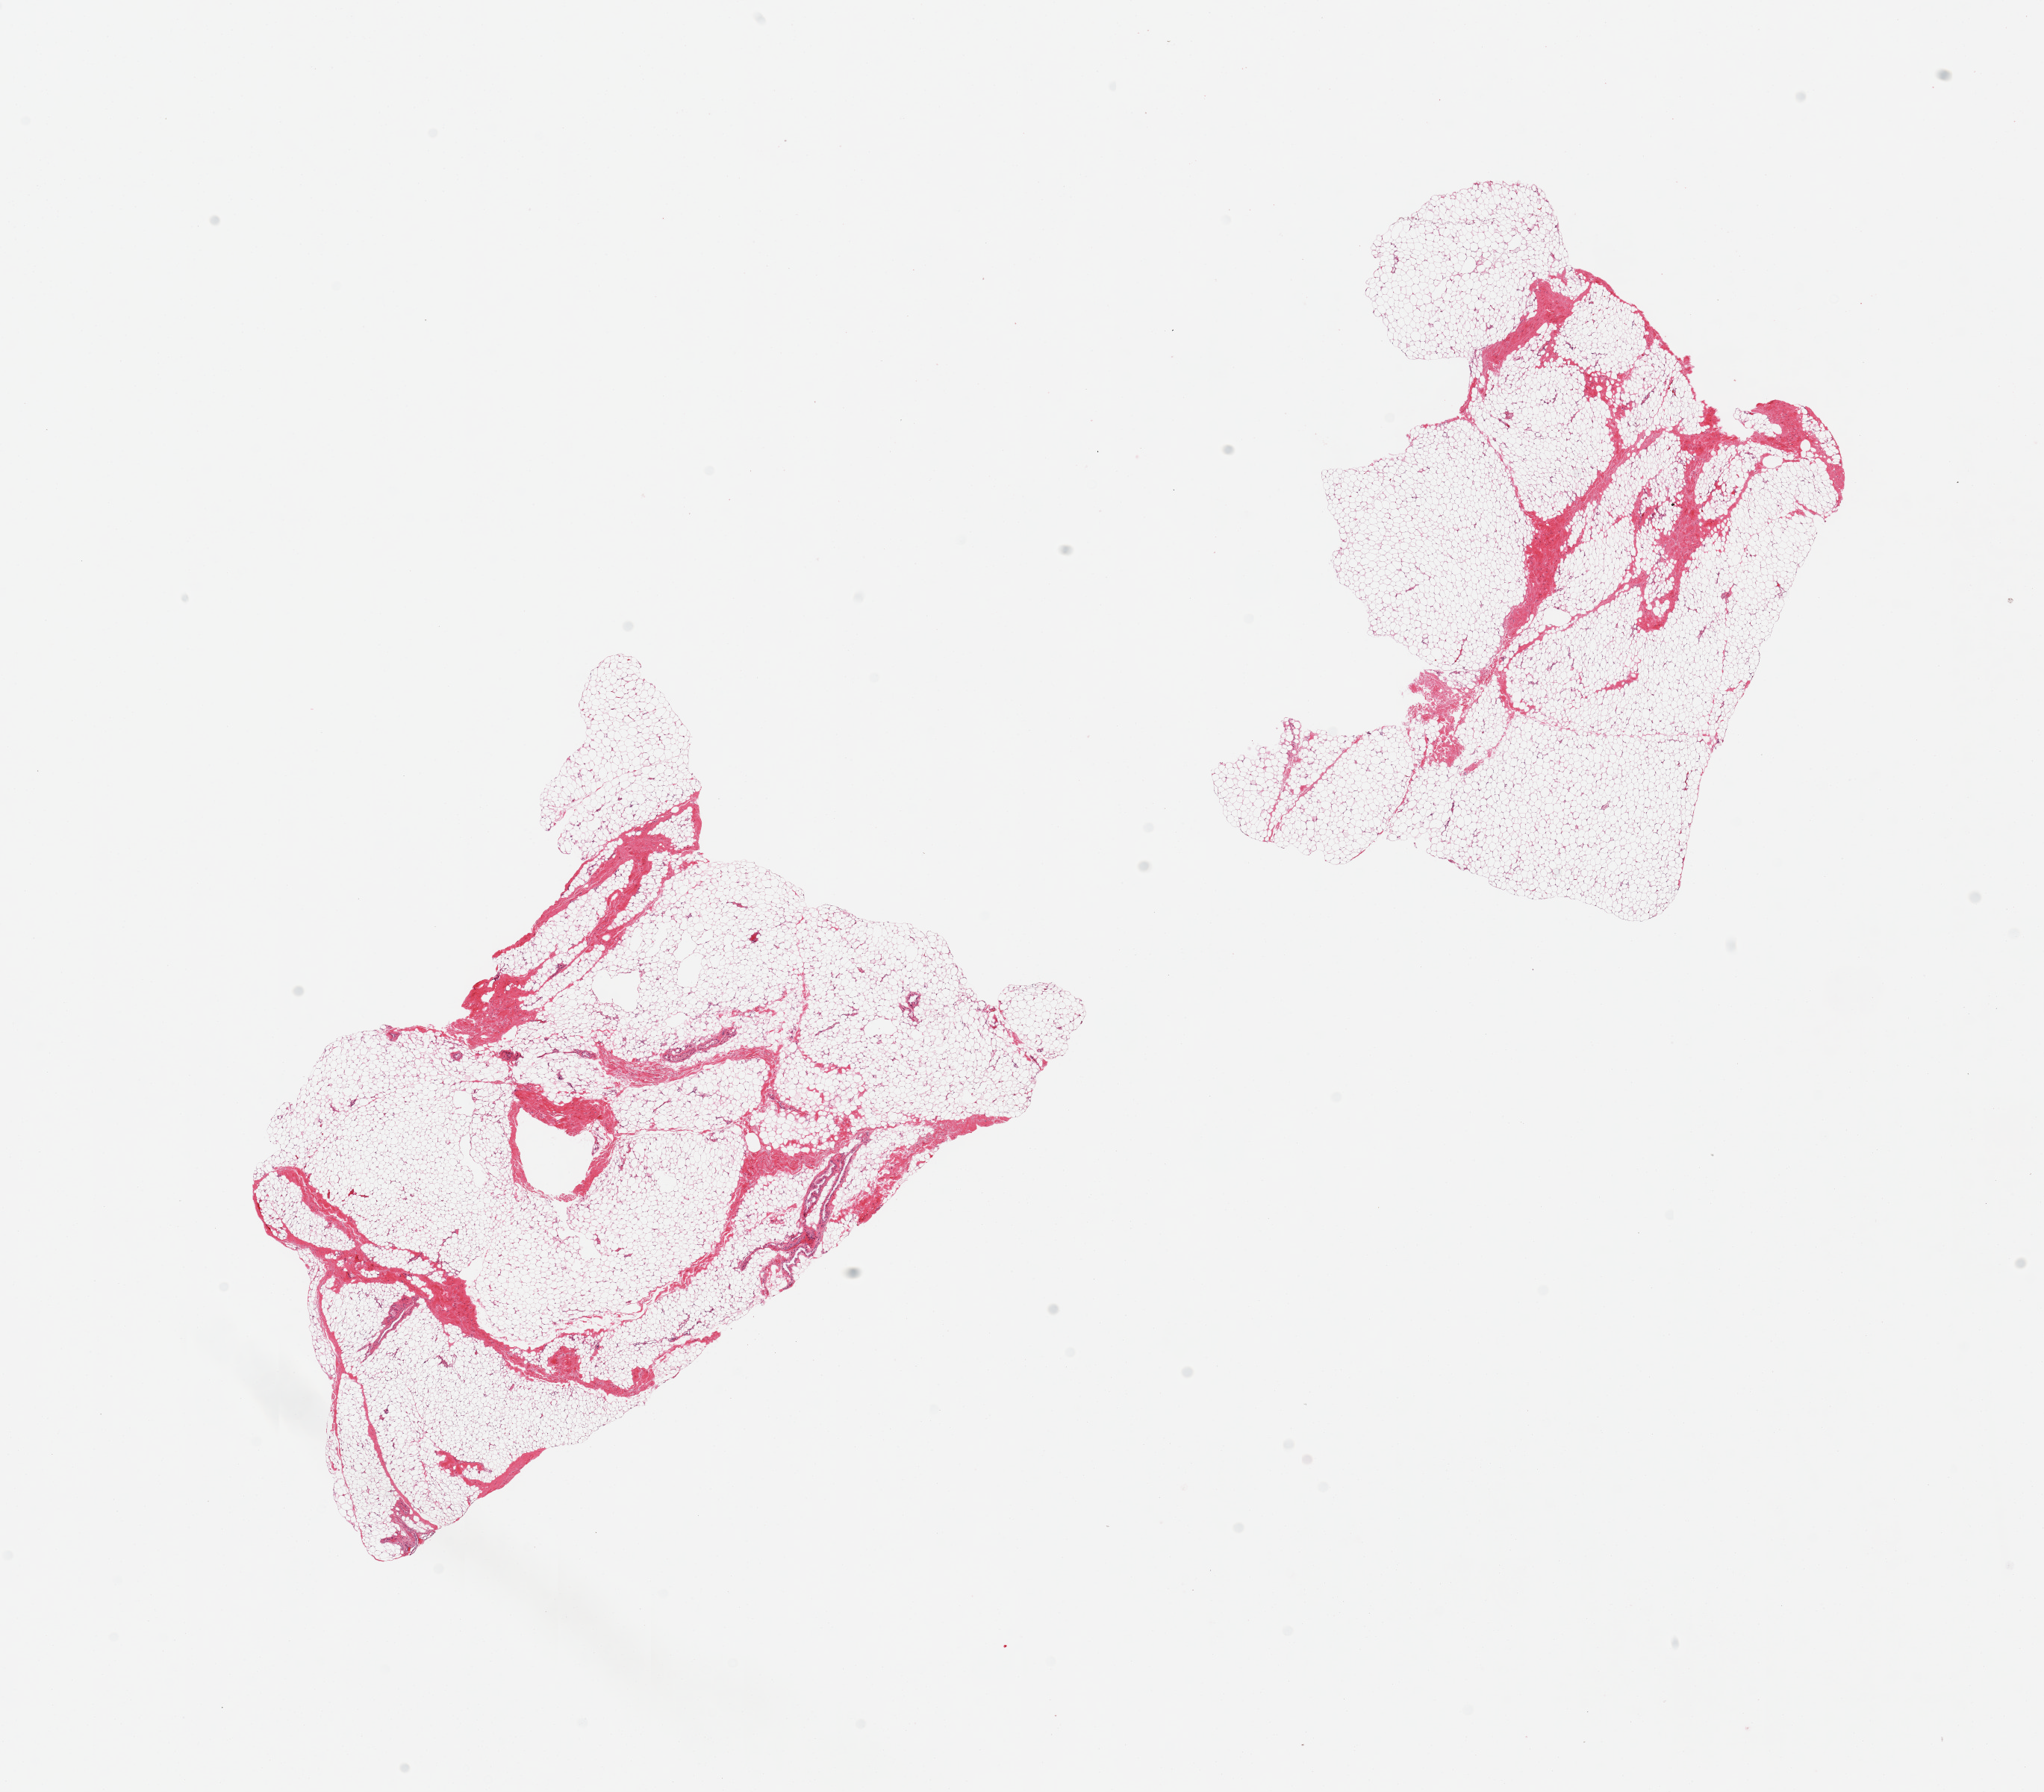
Haematoxylin and eosin whole-slide image, low-resolution overview of the scanned area, about 21.7 x 19.0 mm, PAXgene-fixed paraffin-embedded (PFPE) section, section of breast (target tissue), donor tissue sample. Donor sex: male.
Review note (as recorded): 2 pieces; predominantly fat with limited fibrous stroma (up to 10%).